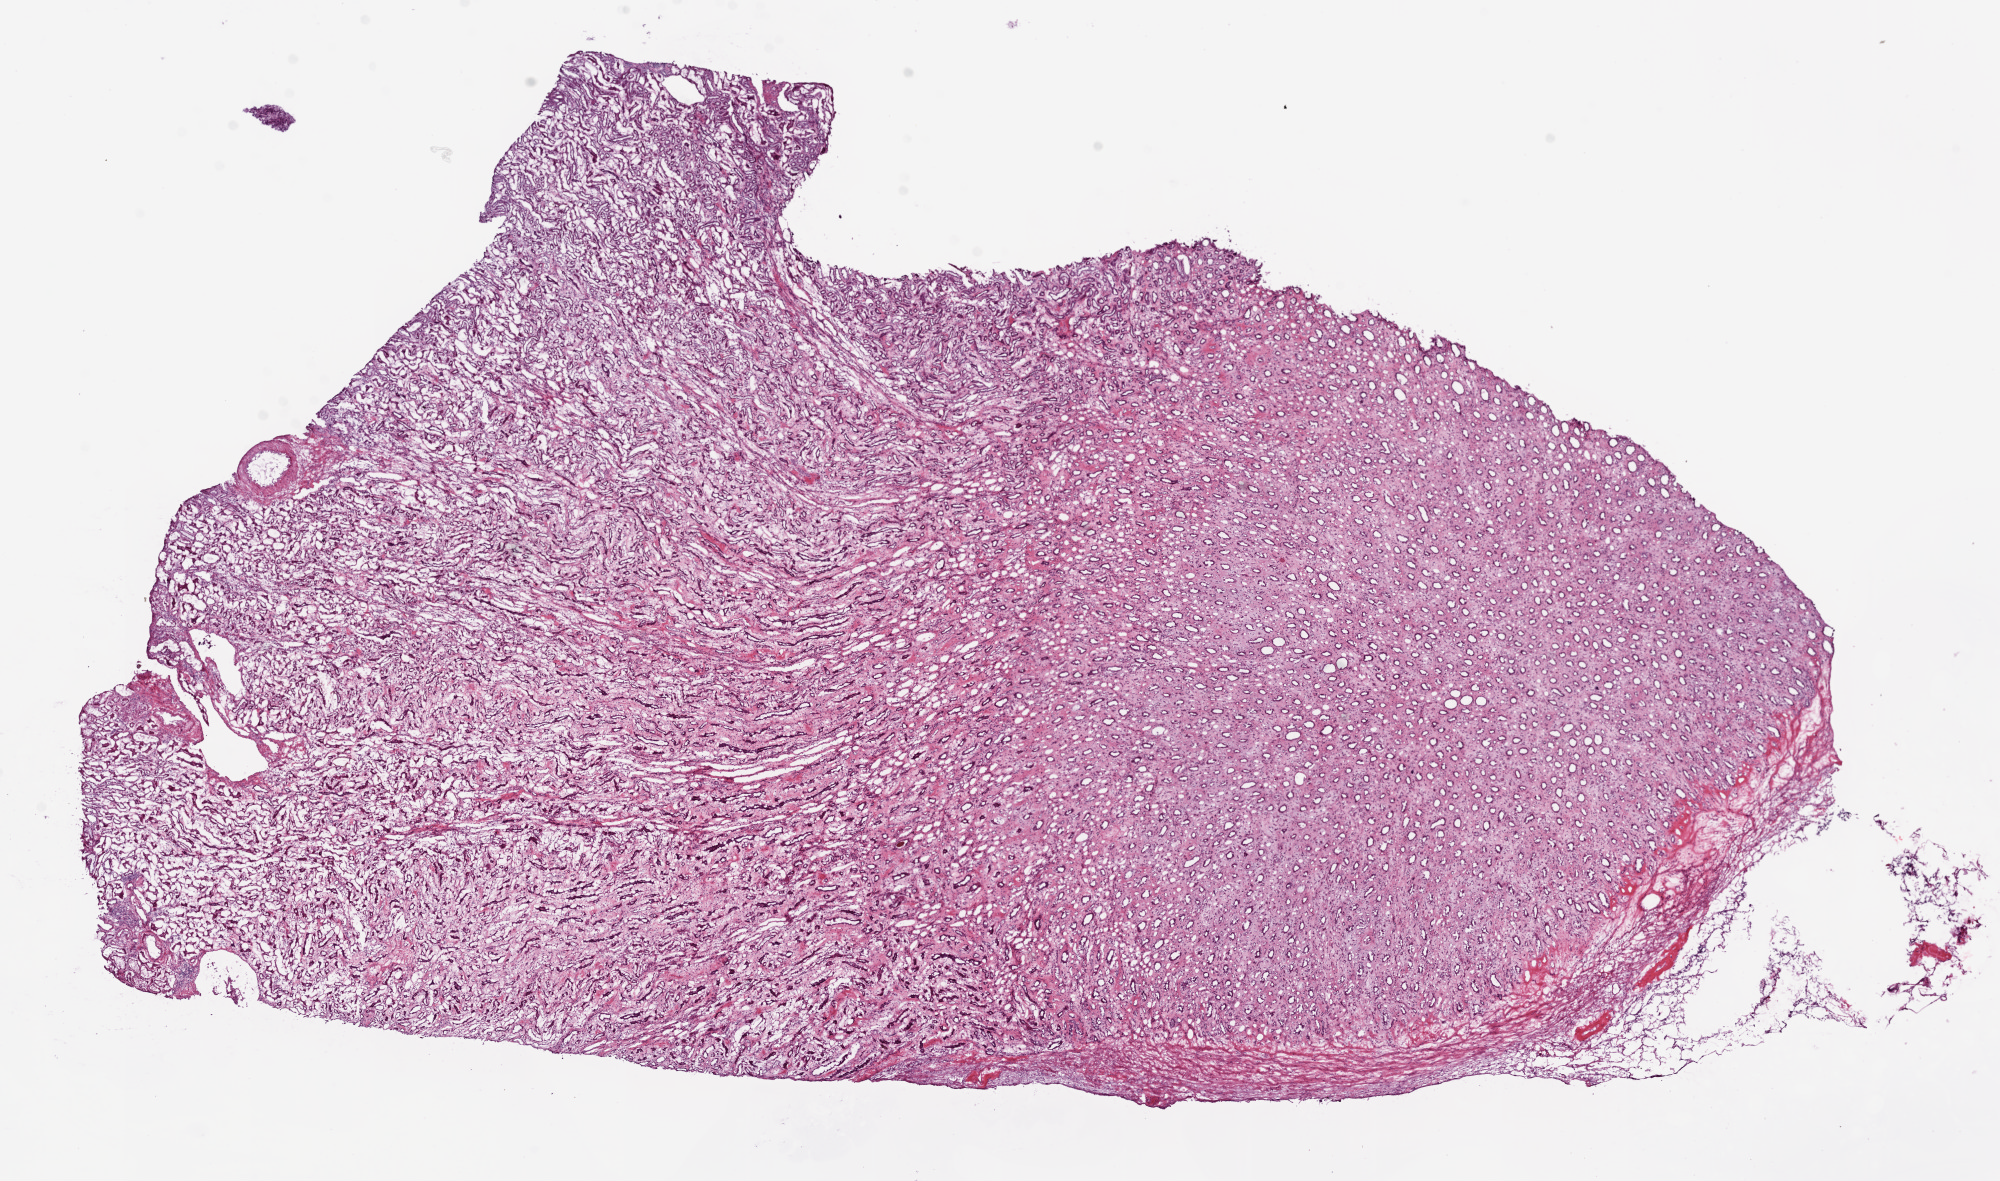
Digitized H&E tissue section (whole slide) — low-resolution overview of the scanned area, about 16.0 x 9.5 mm; frozen section from the bottom of the tissue portion; kidney, solid tissue normal (non-tumour tissue) sample. Male, age 46 years at initial diagnosis.
• this section: solid tissue normal (non-tumour) sample from the same patient
• patient diagnosis: Clear cell adenocarcinoma, NOS